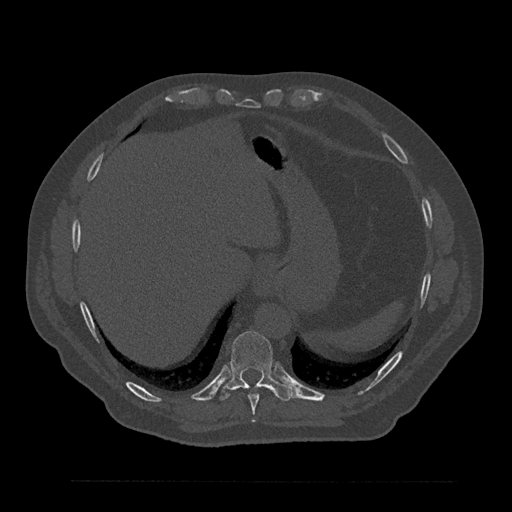
CT including the spine, one axial slice. Slice 370 of 797 in the series (ordered by position). 120 kVp. Bone window (W 1800 / L 400 HU). 0.5 mm slice thickness. 512 × 512 image matrix. Patient: male, 61 years. Case-level facts recorded for this patient, not image findings: primary cancer: prostate.
Outlined on this slice (semi-automatic segmentation, software-assisted and operator-edited):
- T10 vertebra: bounding box (x1, y1, x2, y2) in pixels: (220, 331, 293, 402)
- T9 vertebra: (248, 385, 265, 422)